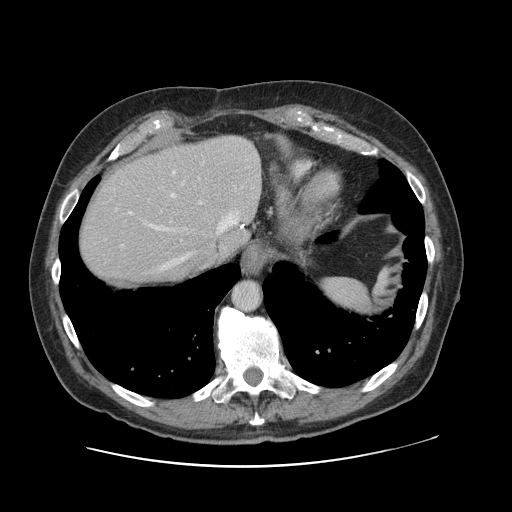
Contrast-enhanced abdominal CT, one axial slice. Slice 98 of 138 in the series (ordered by position). 120 kVp. Intravenous contrast given. Soft-tissue window (W 400 / L 40 HU). 512 × 512 image matrix, field of view 402 × 402 mm. Male patient, age 71 years. From the clinical record (not read from this slice): diagnosis: colorectal cancer liver metastases, imaged before liver resection; multiple liver metastases: no.
Structures marked on this image (manually delineated by an expert):
- hepatic veins: bounding box (x1, y1, x2, y2) in pixels: (153, 211, 244, 268)
- liver: (78, 136, 261, 287)
- planned liver remnant (the part of the liver to remain after resection): (78, 160, 222, 287)